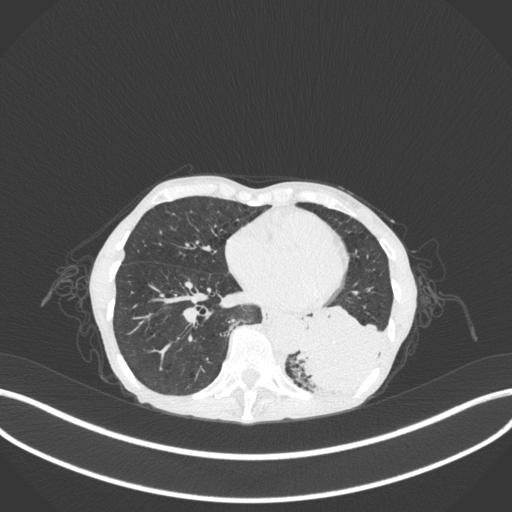
Chest CT, one axial slice; slice 92 of 347 in the series (ordered by position); lung window (W 1500 / L -600 HU); 512 × 512 image matrix, field of view 400 × 400 mm. Patient: female, 70 years. Case-level facts recorded for this patient, not image findings: clinical TNM (as recorded): T3 N0 M0; histopathological grade: G3.
Outlined on this slice (bounding box drawn by a radiologist):
- lung tumour (recorded histology: small cell carcinoma): bounding box [x1, y1, x2, y2] px = [295, 300, 392, 400]